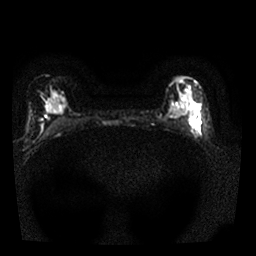
Breast MRI, one axial slice; slice 15 of 25 in the series (ordered by position); diffusion-weighted series; image 2 of 4 stored at this slice position (different b-values; order by instance number); 1.5 T; 4 mm slice thickness; 256 × 256 image matrix, field of view 300 × 300 mm. Female patient.
Structures marked on this image (outlined manually by an expert reader):
- tumour on diffusion-weighted imaging: bounding box [x1, y1, x2, y2] px = [190, 116, 195, 123]